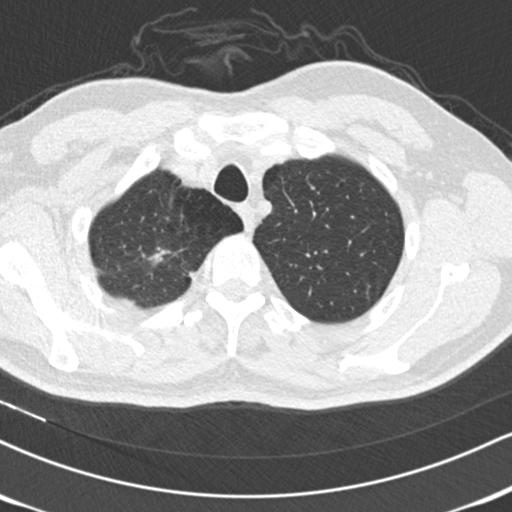
Low-dose screening chest CT, axial slice; second annual screen; lung window (W 1500 / L -600 HU); 2 mm slice thickness; standard (soft-tissue) reconstruction kernel (B30f); slice 30 of 179 in the series; 512 × 512 image matrix. Male participant, aged 56 years at enrolment. Former smoker at enrolment.
Expert-annotated lung lesion, bounding box <129,235,192,281> (left, top, right, bottom; pixels). The exam's reader record, not a measurement of the box and not confirmed to be the same lesion: non-calcified nodule or mass ≥4 mm, right upper lobe, 13 × 10 mm, spiculated (stellate) margins, soft tissue attenuation. Official screen result: positive, other. Later outcome: lung cancer diagnosed 384 days after this screen (after the third annual screen) — adenocarcinoma, NOS, right upper lobe, moderately differentiated (G2), stage IA (AJCC 6th edition), 9 mm at pathology.